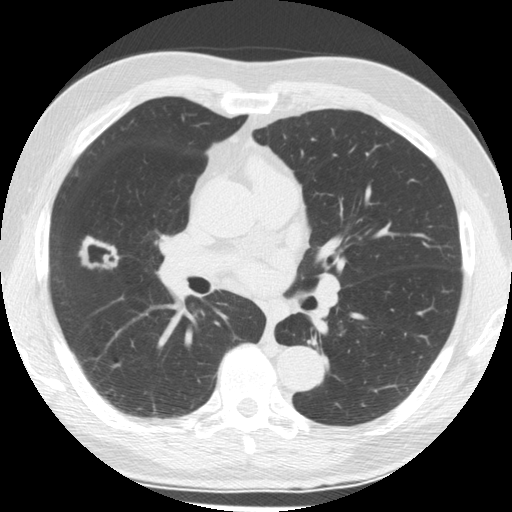
Low-dose screening chest CT, one axial slice. Position 102 of 176 along the scan axis. Reconstruction kernel STANDARD. 120 kVp. Lung window (W 1500 / L -600 HU). 2.5 mm slice thickness. 512 × 512 image matrix, field of view 348 × 348 mm.
Outlined on this slice (outlined manually by an expert reader):
- lesion 1 (tumor, middle lobe of right lung): box from (x=79, y=236) to (x=120, y=269) px